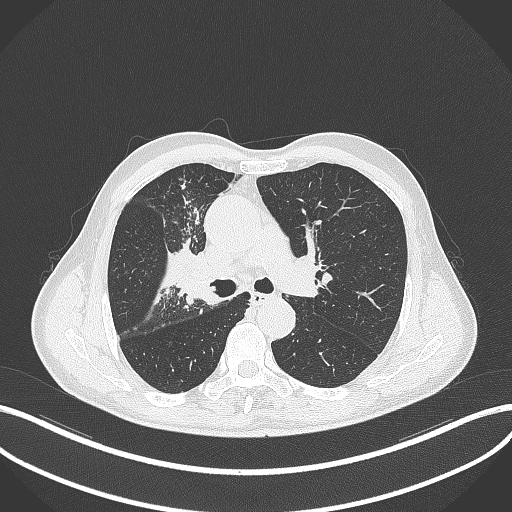
Chest CT, one axial slice. Slice 308 of 490 in the series (ordered by position). Reconstruction kernel B70f. 120 kVp. Lung window (W 1500 / L -600 HU). 1 mm slice thickness. 512 × 512 image matrix, field of view 400 × 400 mm. Patient: male, 69 years. Case-level facts recorded for this patient, not image findings: clinical TNM (as recorded): T2a N0 M0.
Structures marked on this image (rectangle marked by the reading radiologist):
- lung tumour (recorded histology: adenocarcinoma): box from (x=164, y=248) to (x=226, y=307) px